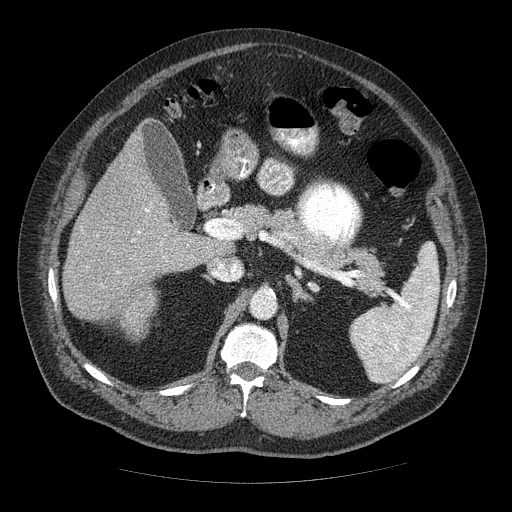
Contrast-enhanced abdominal CT (liver protocol), one axial slice. Slice 28 of 85 in the series (ordered by position). Reconstruction kernel STANDARD. 120 kVp. Soft-tissue window (W 400 / L 40 HU). 2.5 mm slice thickness. 512 × 512 image matrix. From the clinical record (not read from this slice): diagnosis: hepatocellular carcinoma (patient treated with transarterial chemoembolisation; whether this scan precedes or follows treatment is not stated here); TNM stage (as recorded): Stage-IIIA.
Outlined on this slice (semi-automatic segmentation, software-assisted and operator-edited):
- liver parenchyma outside the tumour (the mass and vessels are separate outlines, so this box may not span the whole liver): bounding box (x1, y1, x2, y2) in pixels: (62, 126, 220, 332)
- mass: (121, 289, 155, 334)
- liver vessels: (87, 208, 165, 273)